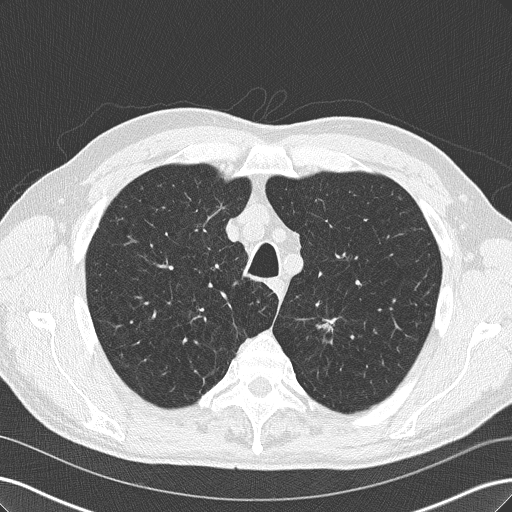
Chest CT (low-dose screening protocol), one axial image, third screening round (two years after baseline), lung window (W 1500 / L -600 HU), 2 mm slice thickness, lung (sharp) reconstruction kernel (B50f), slice 41 of 219 in the series. Male, age 66 years at enrolment.
Expert-annotated lung lesion, bounding box (x1, y1, x2, y2) in pixels: (294, 303, 352, 348). The exam's reader record, not a measurement of the box and not confirmed to be the same lesion: non-calcified nodule or mass ≥4 mm, left upper lobe, 14 × 9 mm, spiculated (stellate) margins, soft tissue attenuation, pre-existing on the prior screen: yes; interval growth: yes. Participant outcome: lung cancer diagnosed 19 days after this screen — squamous cell carcinoma, NOS, left upper lobe, poorly differentiated (G3), stage IA (AJCC 6th edition), 15 mm at pathology.